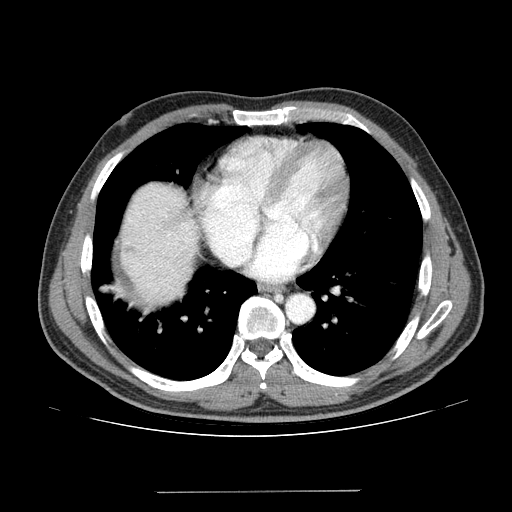
Contrast-enhanced abdominal CT (liver protocol), one axial slice. Slice 123 of 131 in the series (ordered by position). Reconstruction kernel STANDARD. 100 kVp. One of 2 acquisitions stored at this slice position. Soft-tissue window (W 400 / L 40 HU). 2.5 mm slice thickness. 512 × 512 image matrix. Case-level facts recorded for this patient, not image findings: diagnosis: hepatocellular carcinoma (patient treated with transarterial chemoembolisation; whether this scan precedes or follows treatment is not stated here); TNM stage (as recorded): Stage-I; Child-Pugh class: A; tumour differentiation: poorly differentiated; tumour nodularity: uninodular.
Outlined on this slice (semi-automatically segmented with operator editing):
- liver parenchyma outside the tumour (the mass and vessels are separate outlines, so this box may not span the whole liver): bounding box <120,182,198,302> (left, top, right, bottom; pixels)
- mass: <121,244,136,256>
- liver vessels: <130,211,191,244>